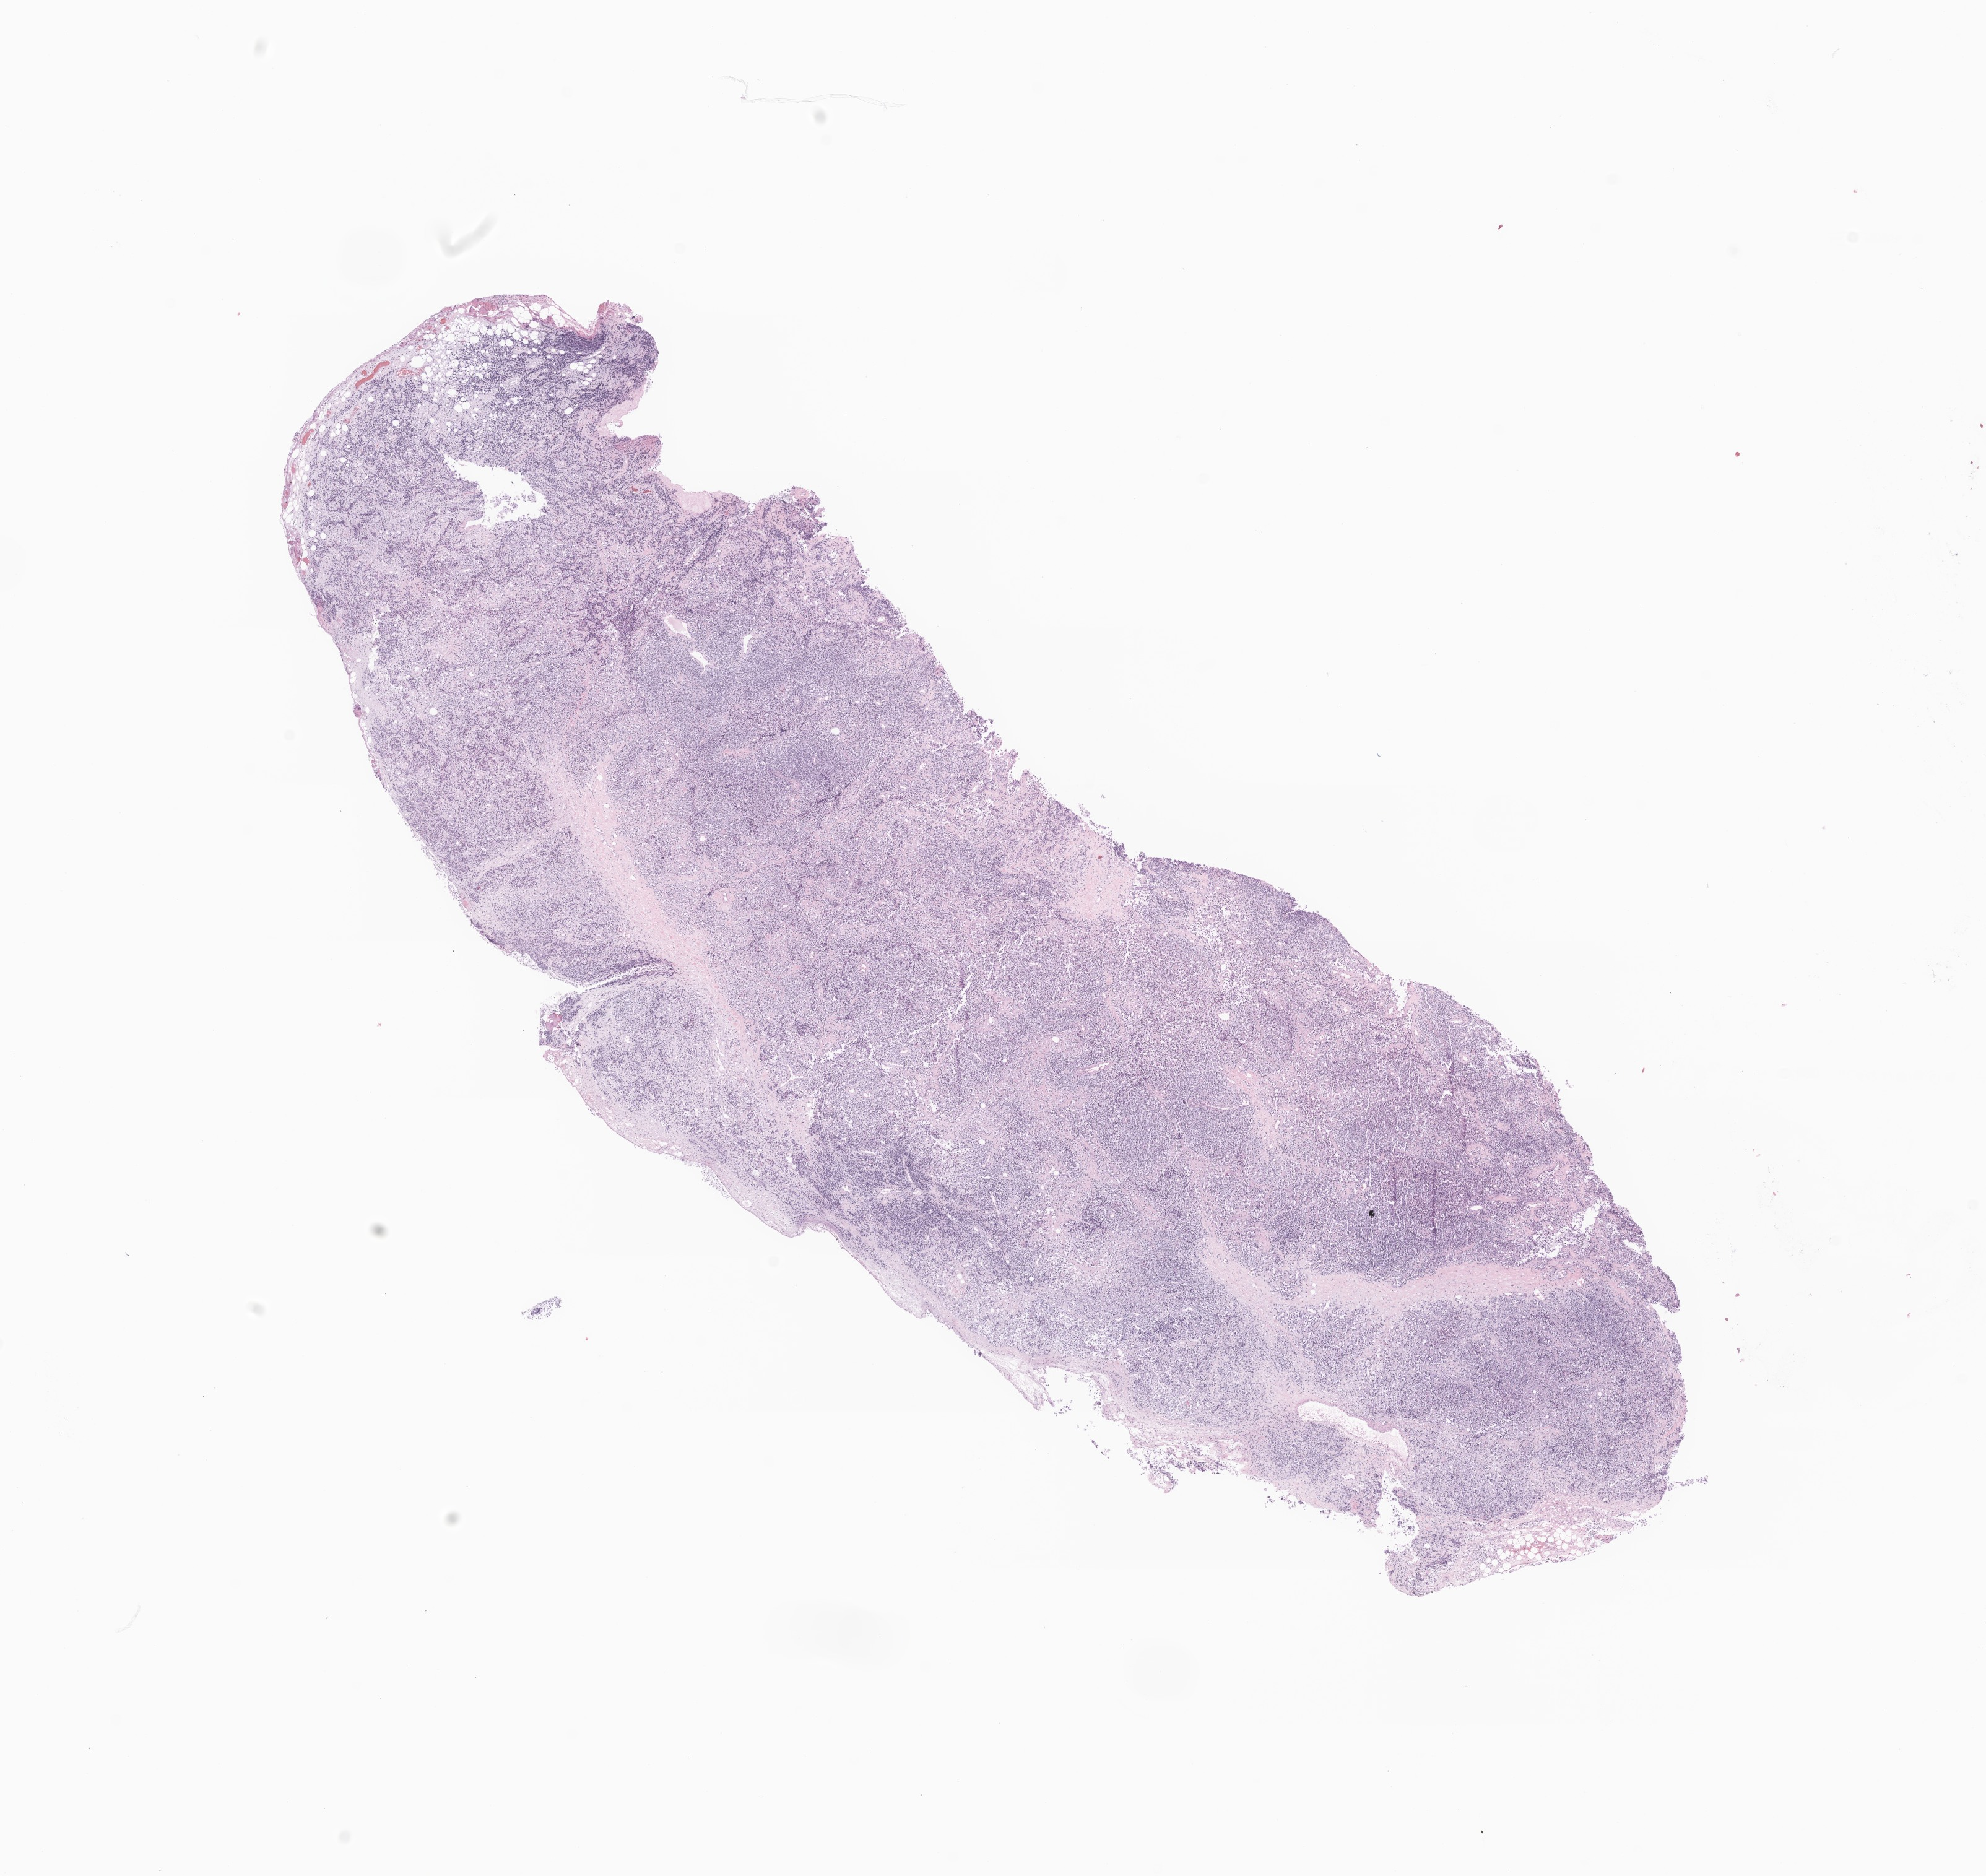
Digitized H&E-stained section of tumor tissue from the anorectal structure, a low-resolution overview of the entire scanned area, about 13.5 x 12.8 mm, formalin-fixed, paraffin-embedded (FFPE) tissue. Patient: female, age 177 months (14 years 9 months).
- recorded diagnosis: Rhabdomyosarcoma, NOS